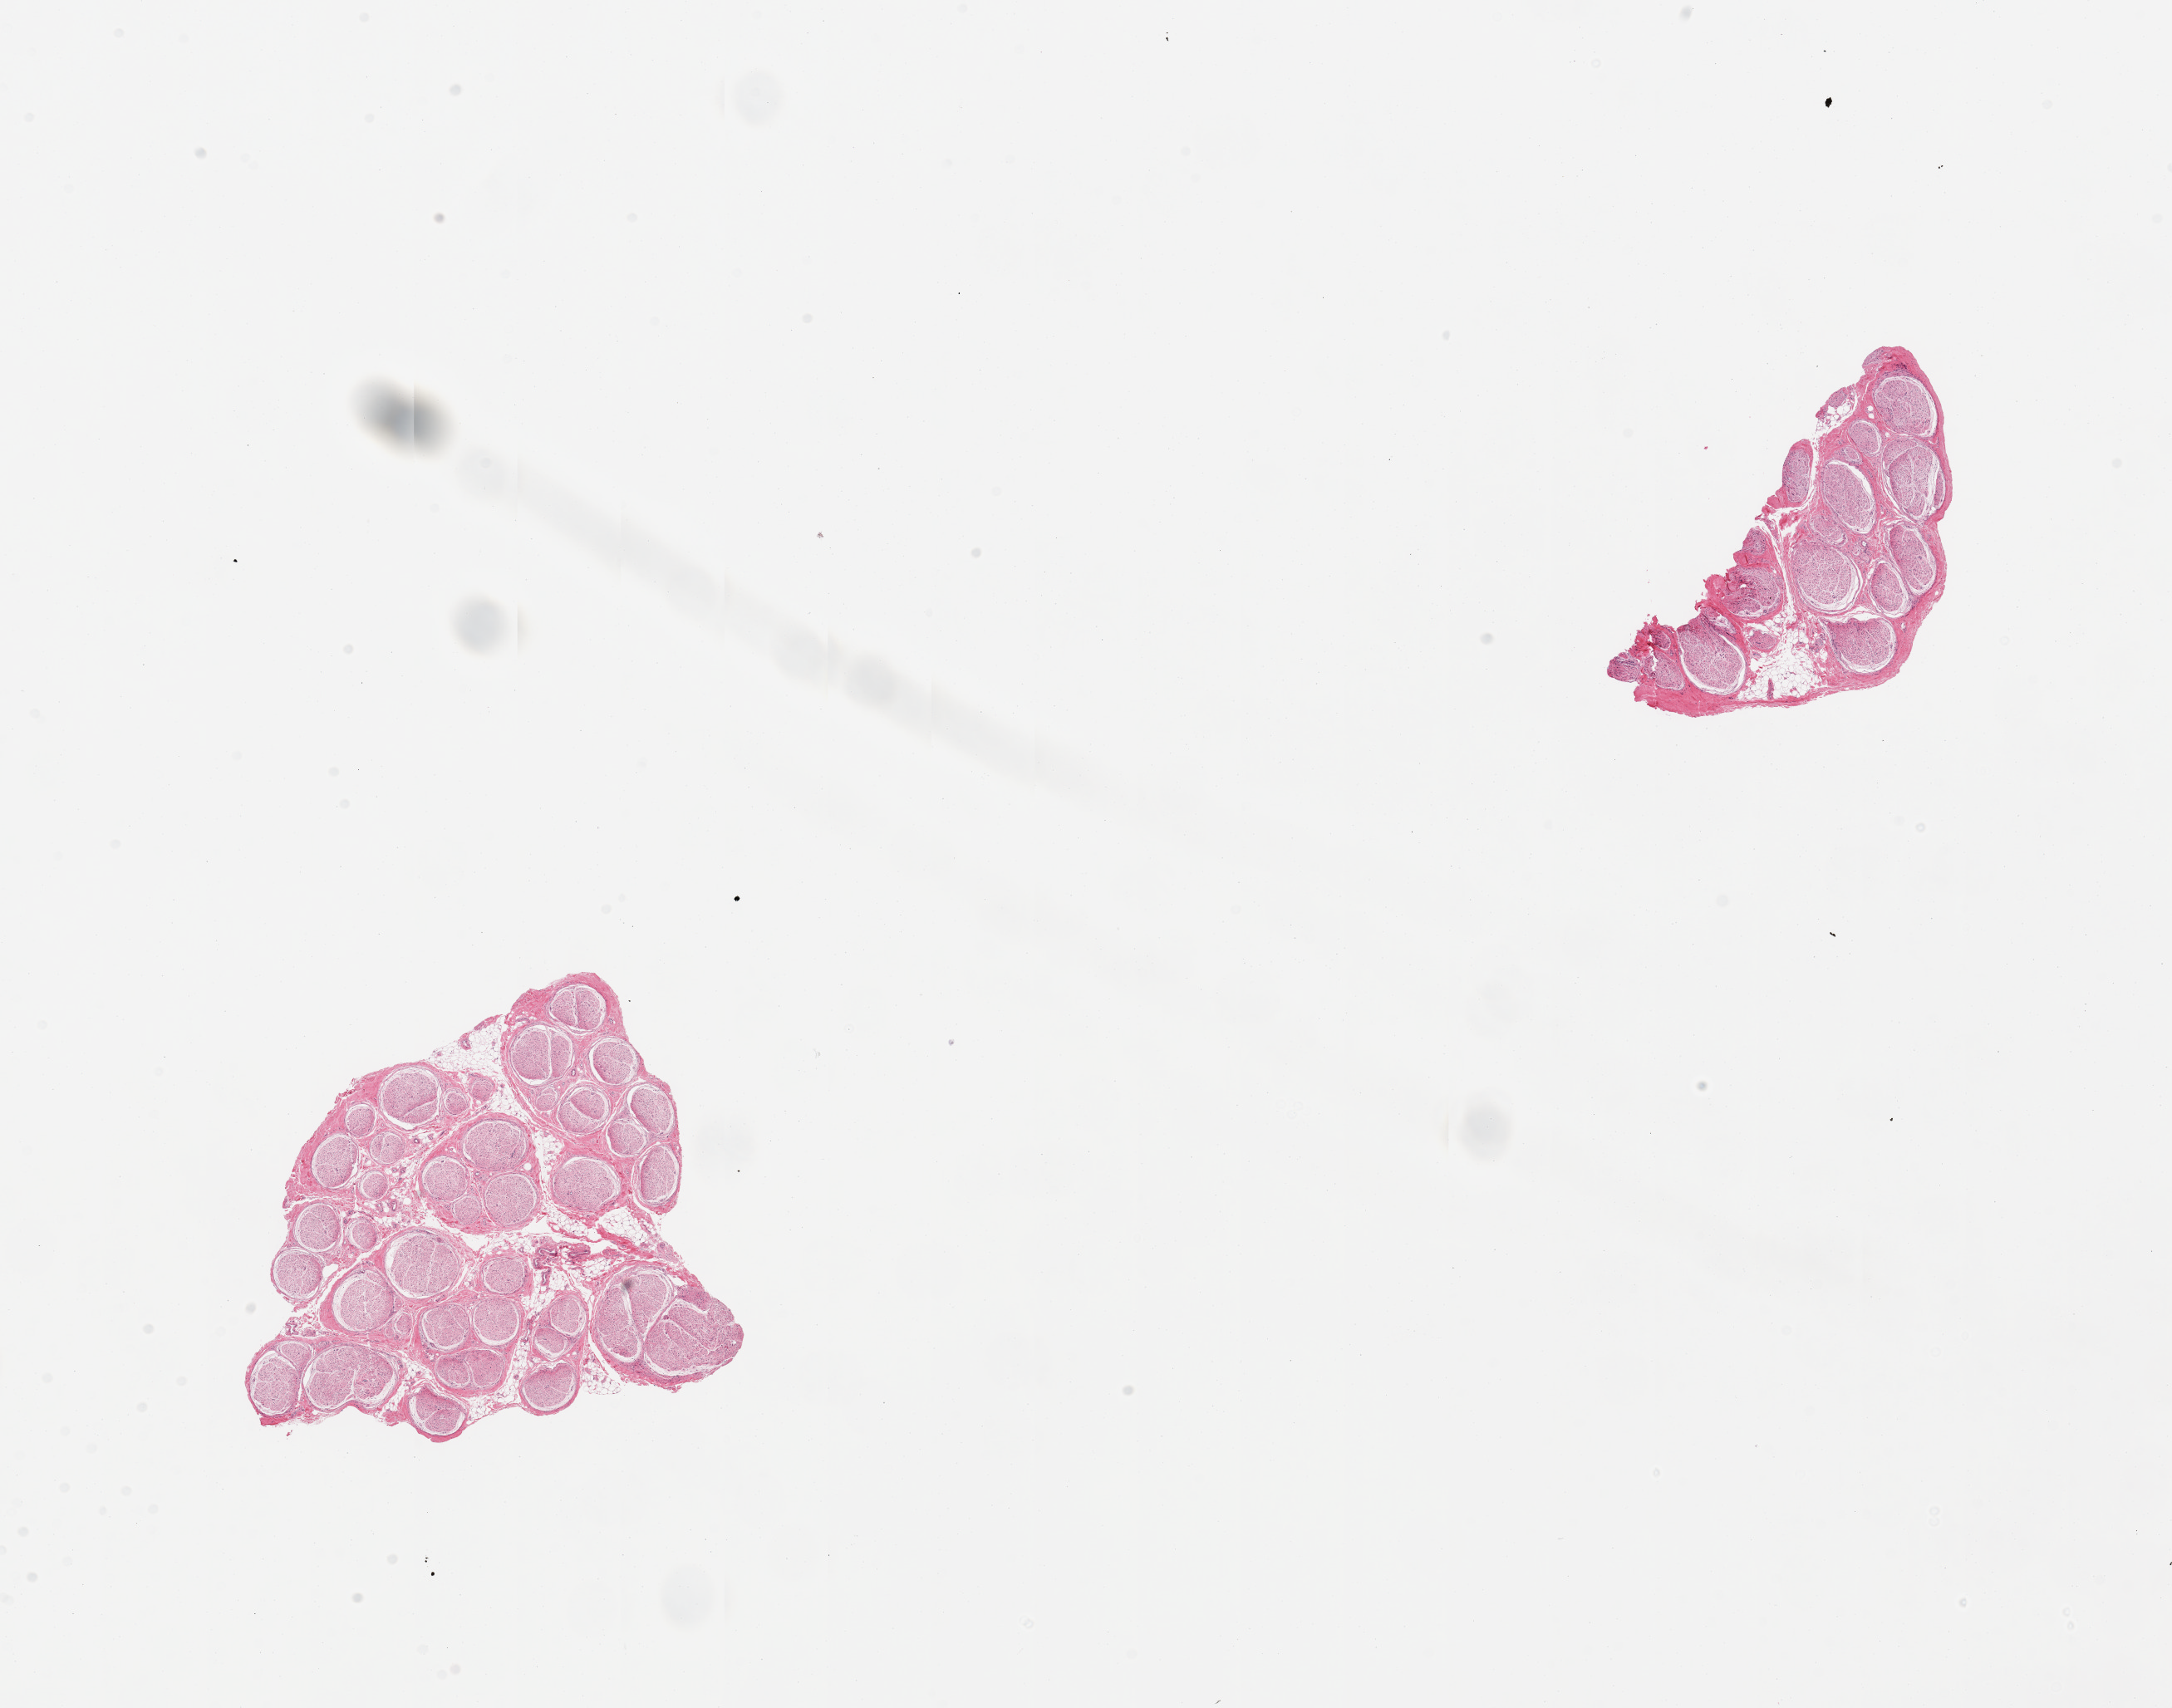
Whole-slide image, H&E stain — a low-resolution overview of the entire scanned area, about 20.7 x 16.3 mm; PAXgene-fixed, paraffin-embedded tissue; section of tibial nerve (target tissue); donor tissue sample.
Review note (as recorded): 2 pieces, no adherent fat, well trimmed, good specimens.